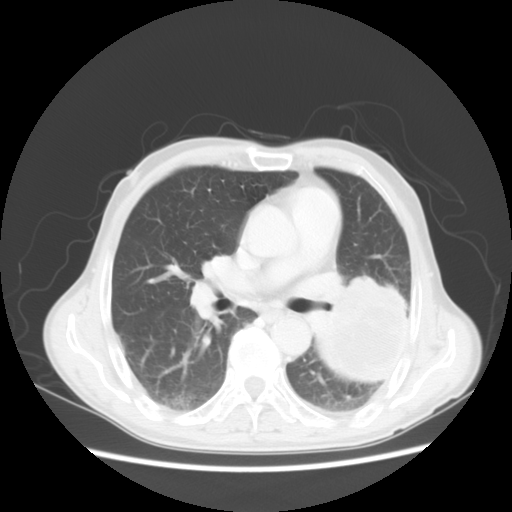
Chest CT, one axial slice. Slice 28 of 51 in the series (ordered by position). Reconstruction kernel STANDARD. Lung window (W 1500 / L -600 HU). 5 mm slice thickness. 512 × 512 image matrix, field of view 360 × 360 mm. Patient: male, 64 years. Case-level facts recorded for this patient, not image findings: clinical TNM (as recorded): T4 N0 M0.
Outlined on this slice (rectangle marked by the reading radiologist):
- lung tumour (recorded histology: squamous cell carcinoma): box from (x=301, y=269) to (x=423, y=387) px